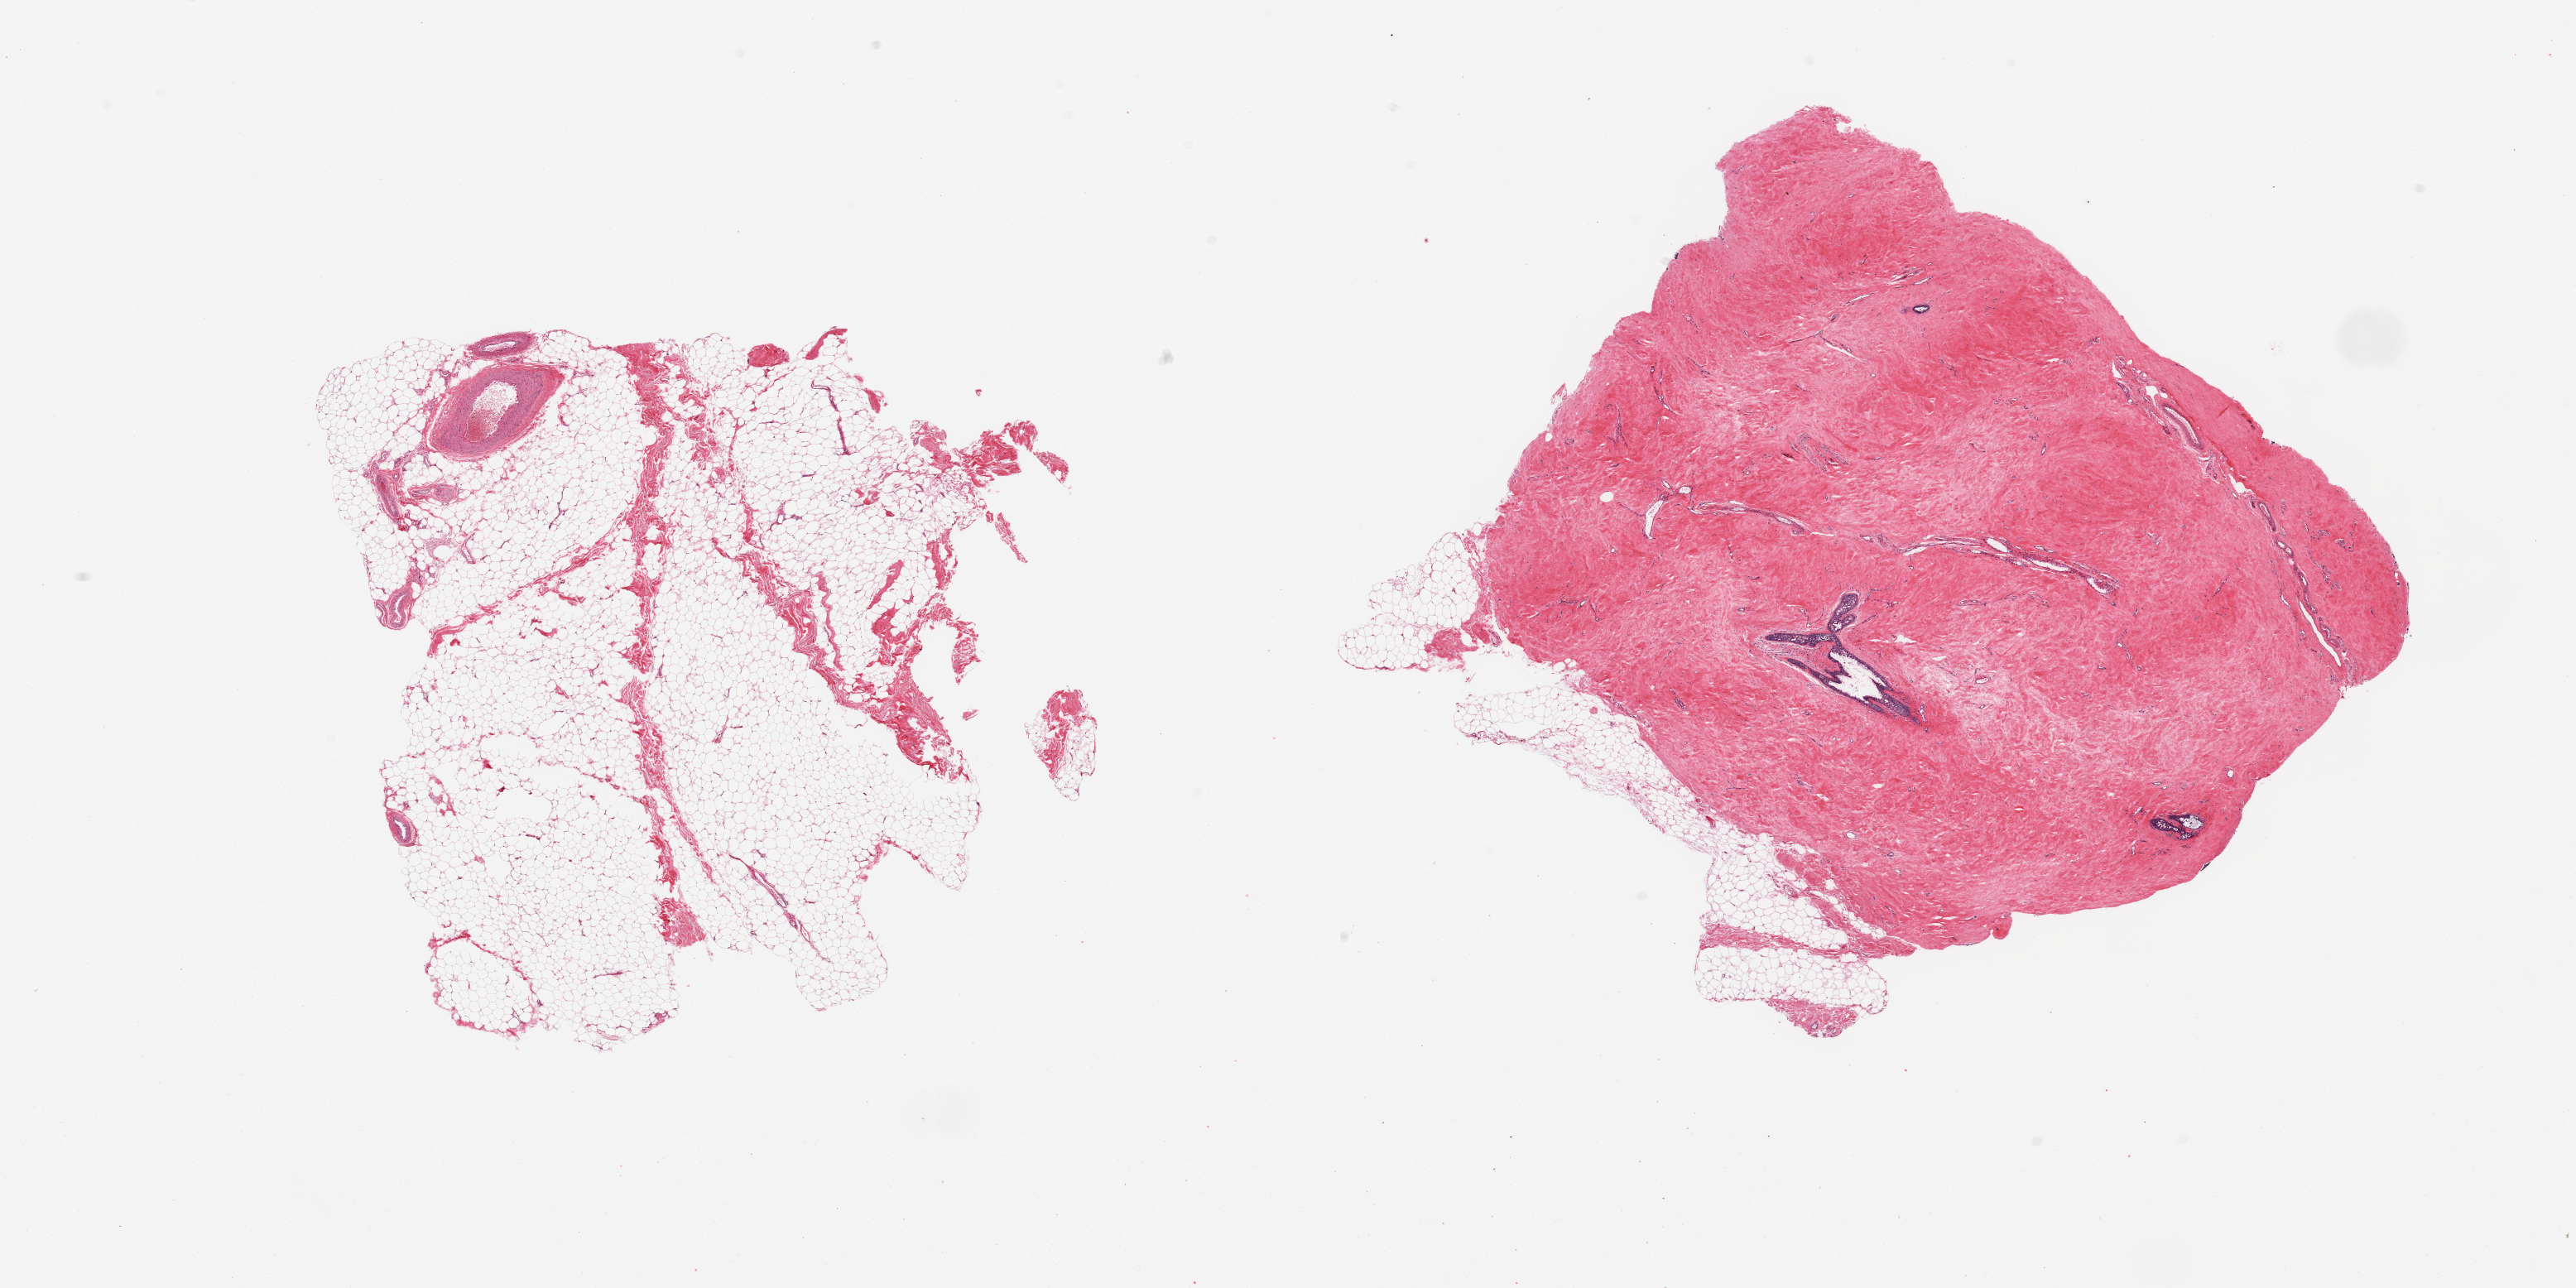
Whole-slide image, haematoxylin and eosin stain, low-resolution overview of the scanned area, about 24.6 x 12.3 mm (from a 20x scan), PAXgene-fixed paraffin-embedded (PFPE) section, section of breast (target tissue), tissue donor sample.
Pathologist's review note for this sample: 2 pieces; 1 piece has dense fibrous stroma and mammary ductal hyperplasia (gynecomastoid changes); other piece is fat with 5% fibrovascular content.